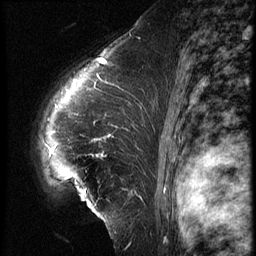
Breast MRI (dynamic contrast-enhanced), one sagittal slice; position 44 of 62 along the scan axis; 3 images stored at this slice position (order not interpretable as contrast timing); 1.5 T; TE 4.2 ms, TR 9 ms; 2.5 mm slice thickness; 256 × 256 image matrix, field of view 180 × 180 mm. Female patient, age 39 years. From the clinical record (not read from this slice): setting: breast cancer imaged before/during neoadjuvant chemotherapy; receptor status: HER2-positive.
Annotated regions visible in this slice (semi-automatically segmented with operator editing):
- analysis volume of interest (the breast-tissue region the enhancement analysis was run in; not a lesion): bounding box <32,64,152,228> (left, top, right, bottom; pixels)
- tumour enhancement mask (voxels above the 140 % enhancement threshold inside the analysis volume of interest): <93,80,135,155>